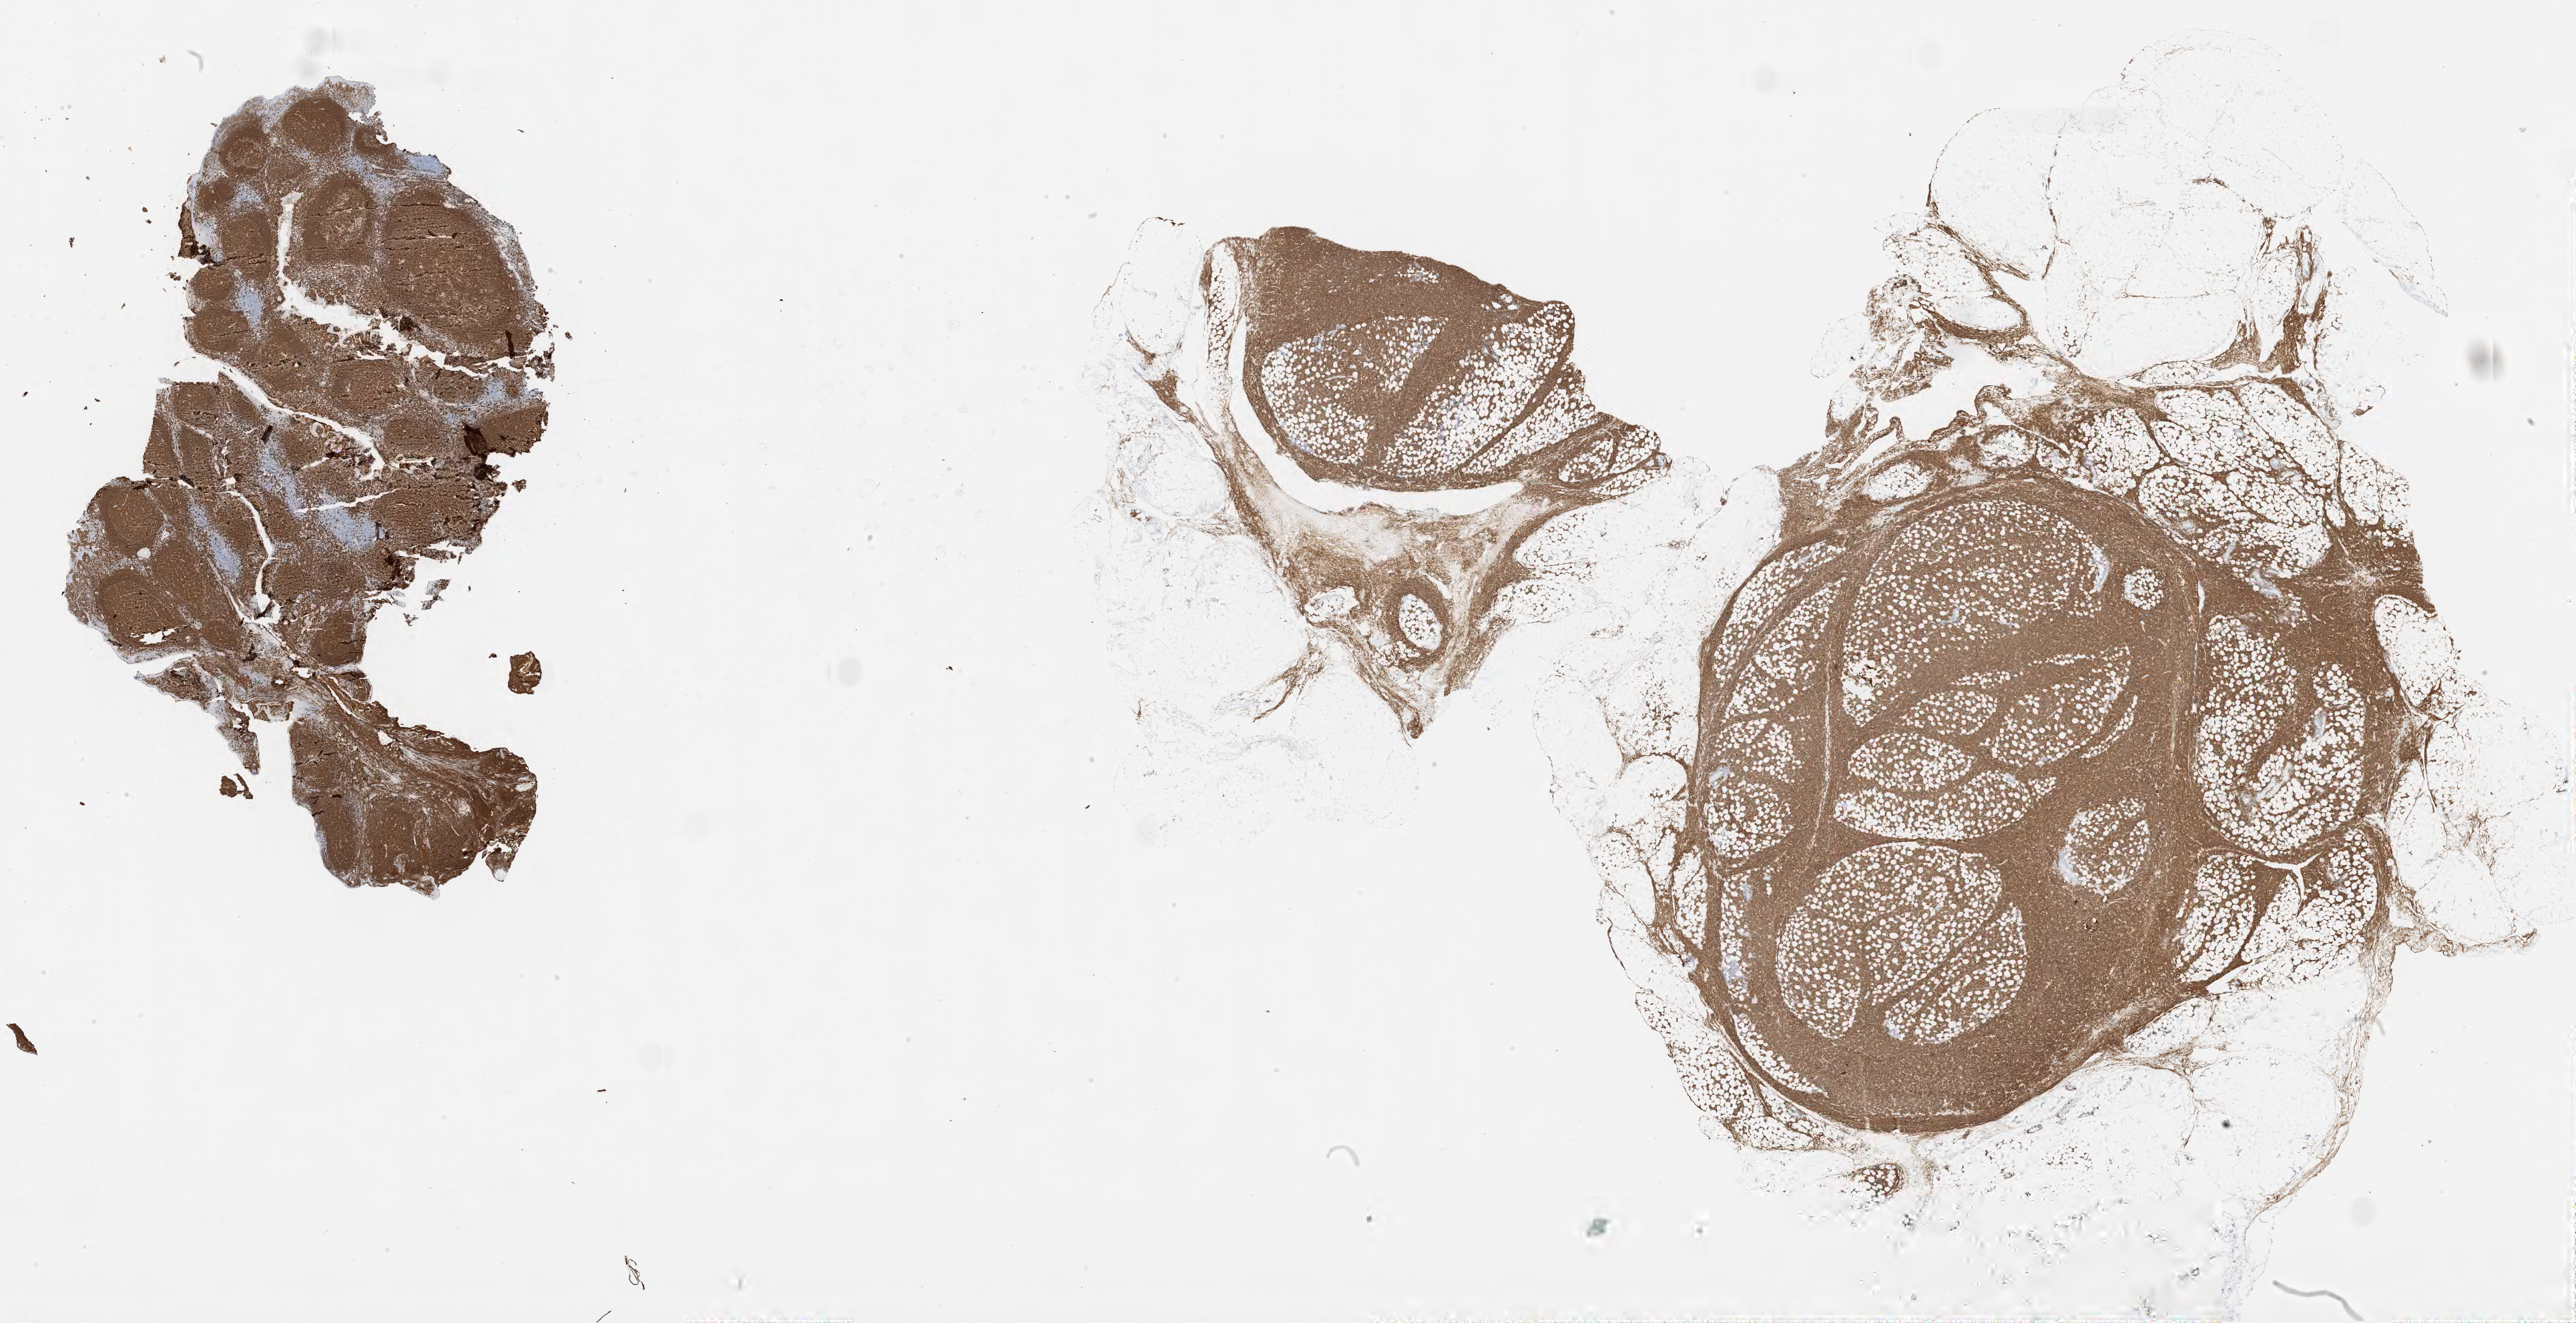
Immunohistochemistry (IHC) whole-slide image stained for CD20, a low-resolution overview of the entire scanned area, about 31.0 x 15.9 mm. Specimen: tumor tissue. Patient male; age 24 years.
• diagnosis: Burkitt lymphoma, NOS